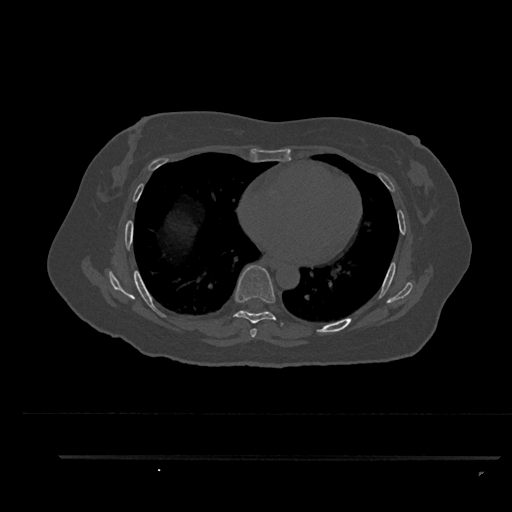
CT including the spine, one axial slice; slice 506 of 797 in the series (ordered by position); 120 kVp; bone window (W 1800 / L 400 HU); 512 × 512 image matrix, field of view 408 × 408 mm. Female patient, age 44 years. From the clinical record (not read from this slice): primary cancer: renal; vertebrae with lytic lesions (as recorded): L1.
Annotated regions visible in this slice (semi-automatic segmentation, software-assisted and operator-edited):
- T6 vertebra: bounding box (x1, y1, x2, y2) in pixels: (250, 328, 257, 338)
- T7 vertebra: (233, 265, 283, 325)